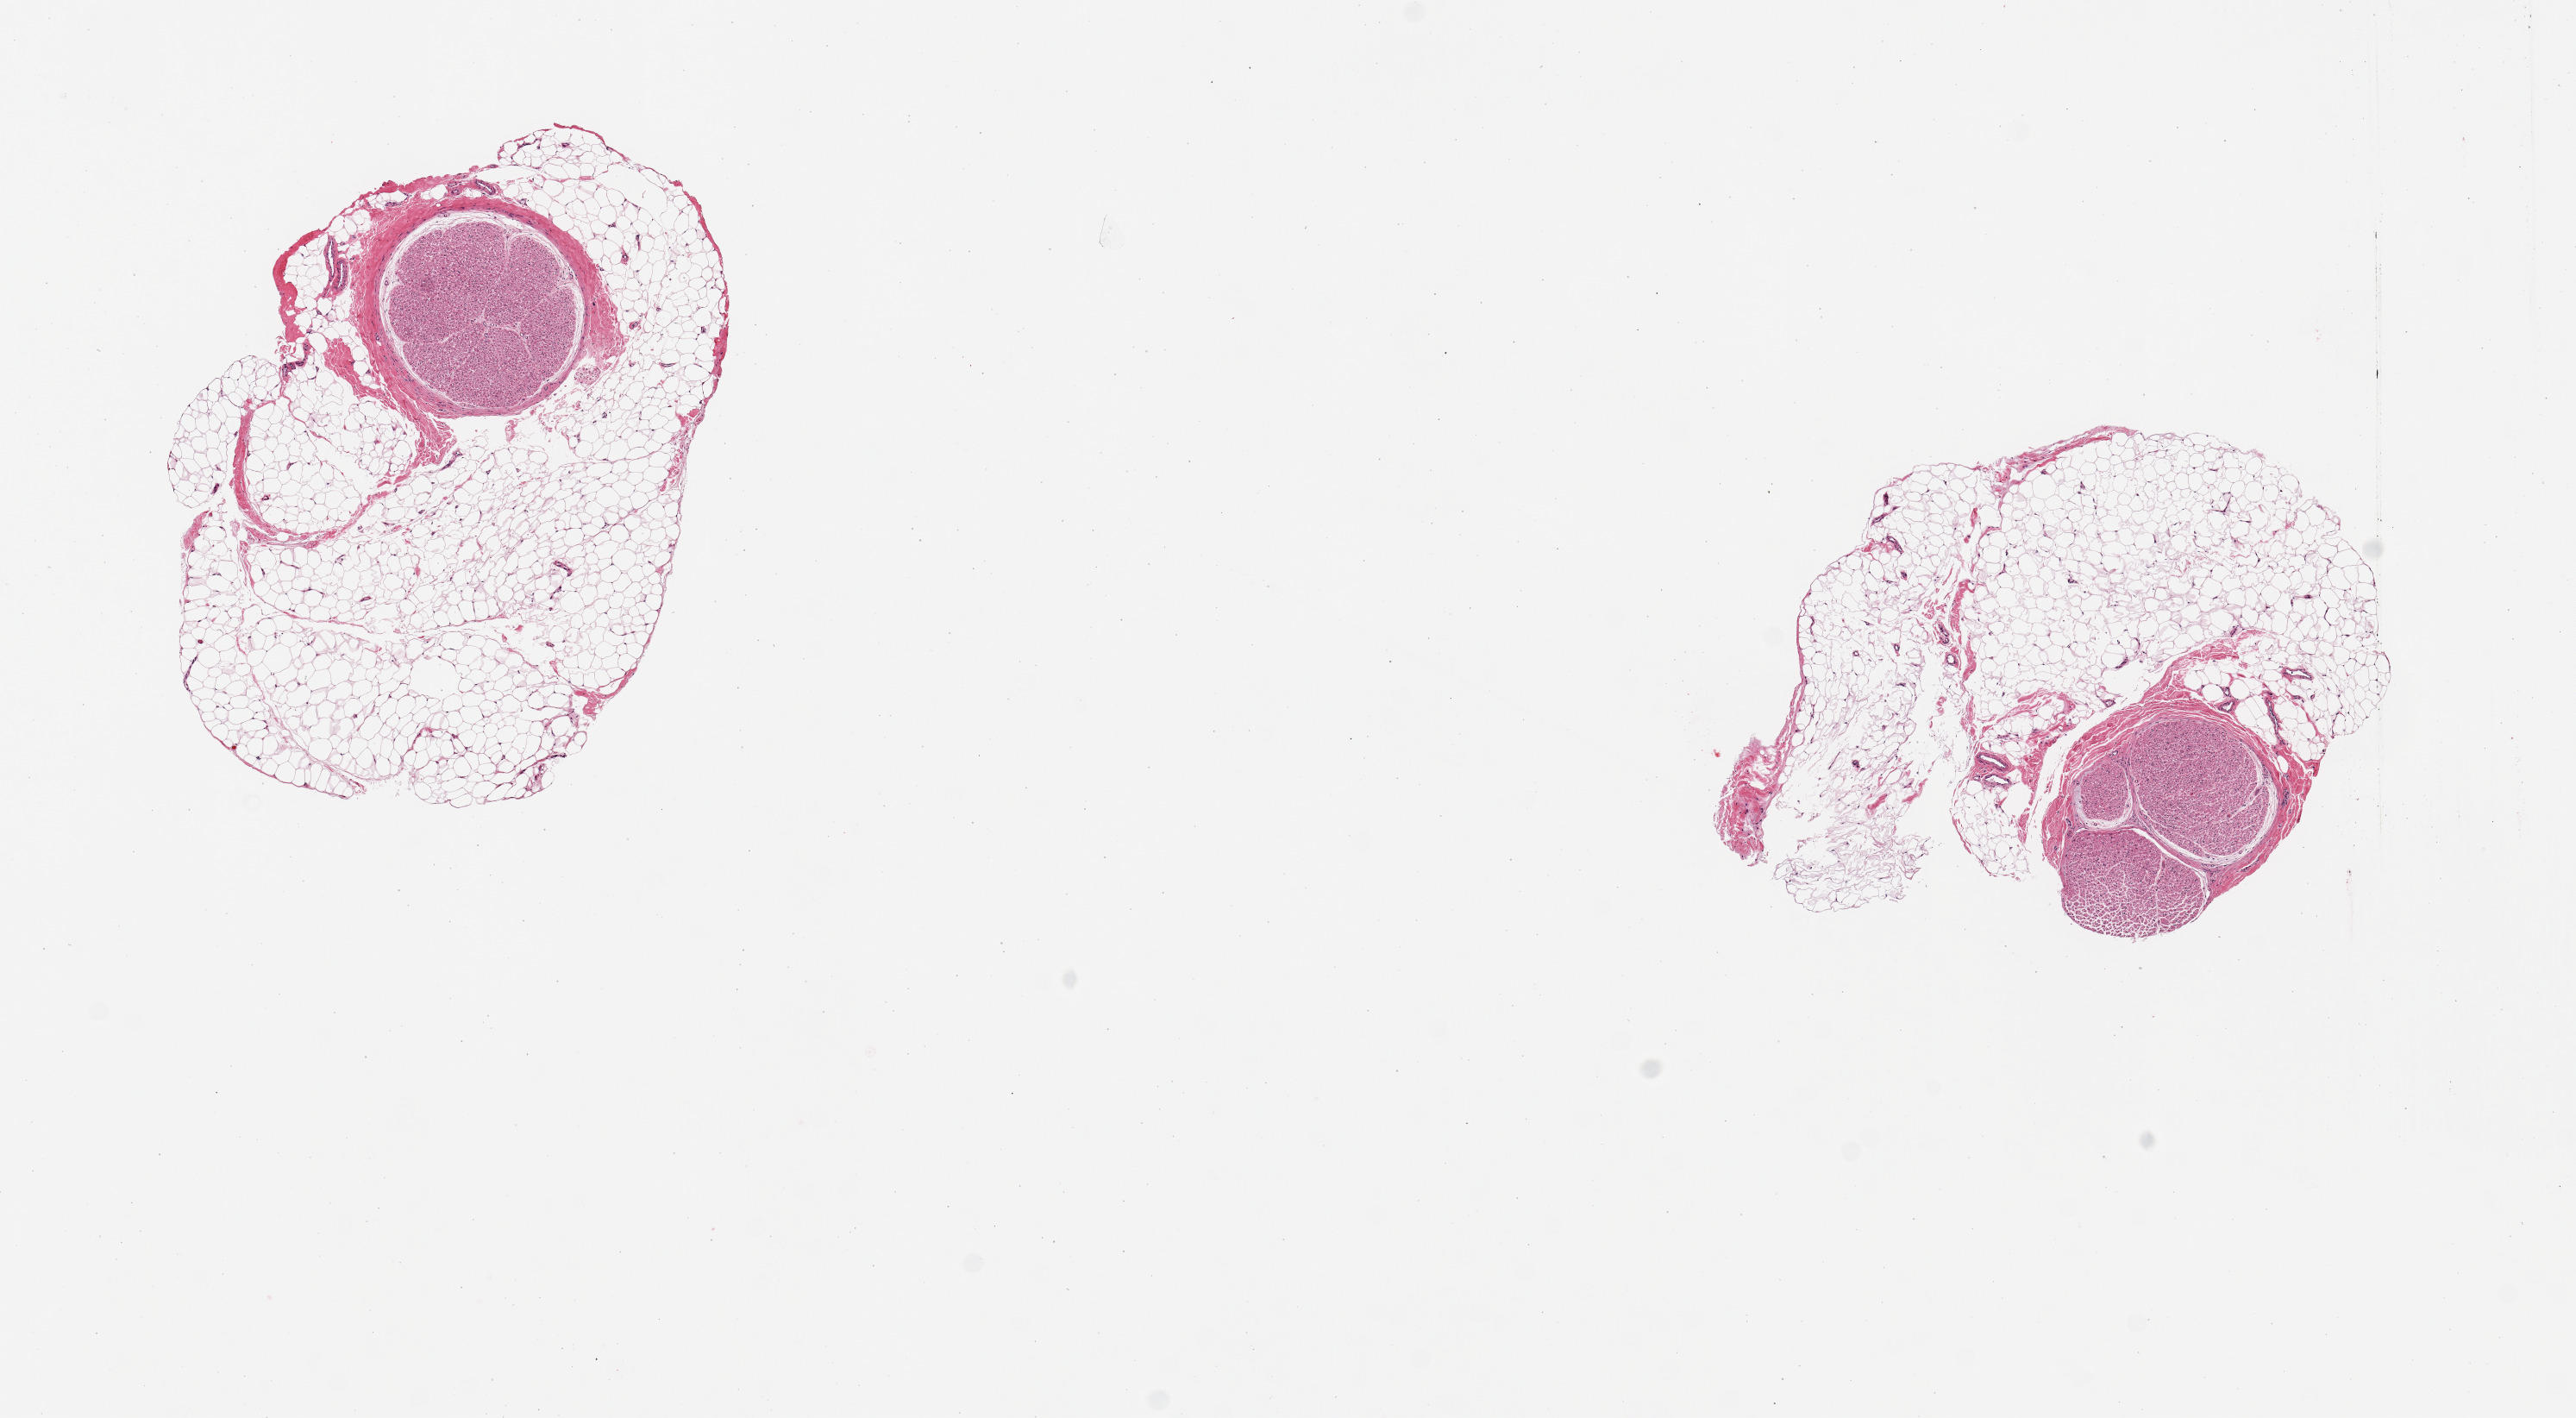
Digitized haematoxylin and eosin-stained section, low-resolution overview of the scanned area, about 11.8 x 6.5 mm (acquisition: 20x scan); PAXgene-fixed, paraffin-embedded tissue; sampled site (target tissue): tibial nerve; tissue donor sample. Female donor.
Review note (as recorded): 2 pieces; external fat comprises 80%.